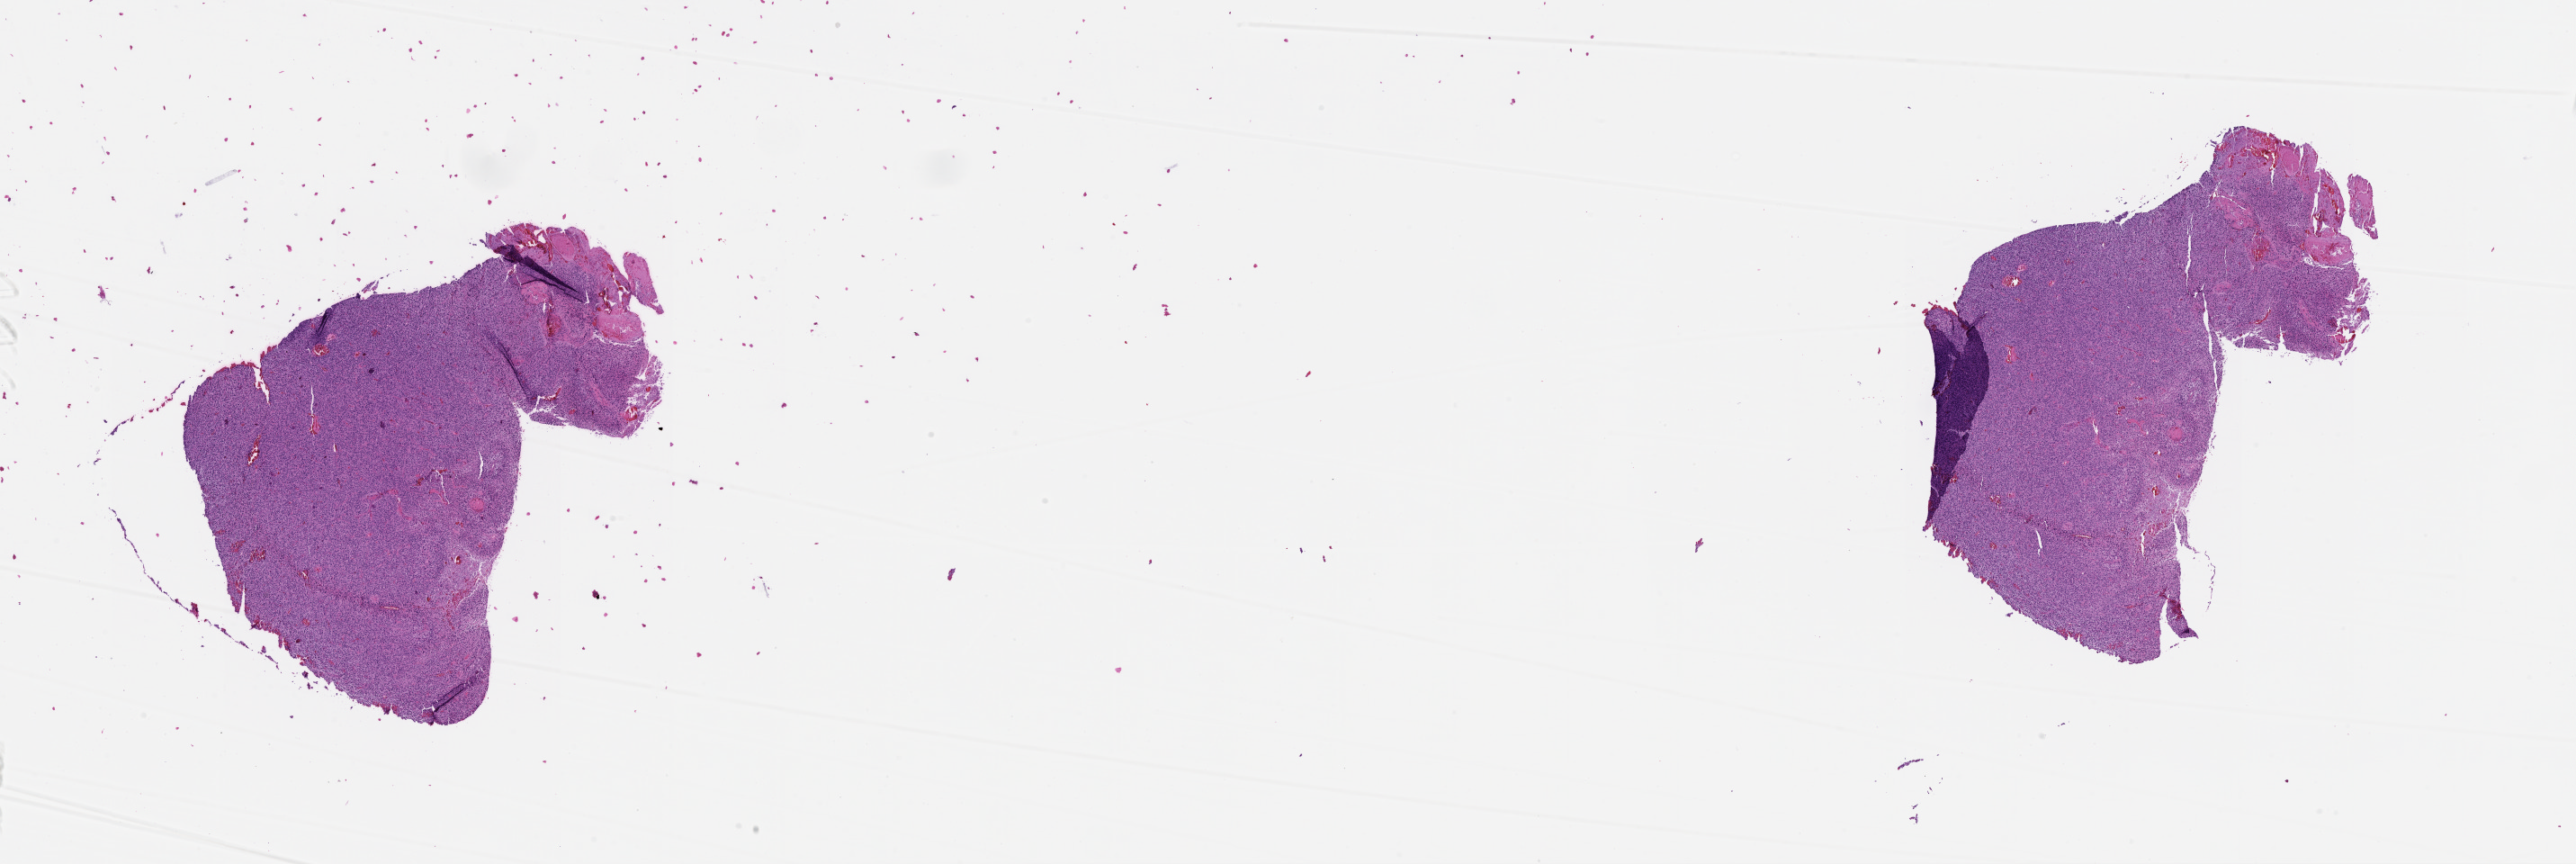
H&E-stained whole-slide image — a low-resolution overview of the entire scanned area, about 23.1 x 7.7 mm. Tumour tissue sample, sampled site: brain. 71-year-old female patient. Pathologist review of this section (percent, as recorded): tumour nuclei 85%, necrosis 5%.
- primary tumour site (as recorded): frontal lobe
- histologic diagnosis: Glioblastoma